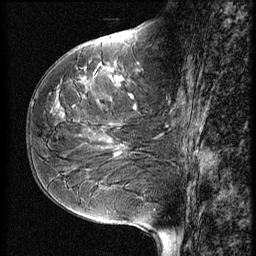
Breast MRI (dynamic contrast-enhanced), one sagittal slice; position 28 of 56 along the scan axis; 3 images stored at this slice position (order not interpretable as contrast timing); 1.5 T; TE 4.2 ms, TR 9 ms; 256 × 256 image matrix, field of view 180 × 180 mm. Patient: female, 51 years. From the clinical record (not read from this slice): setting: breast cancer imaged before/during neoadjuvant chemotherapy; receptor status: HR-positive, HER2-negative.
Annotated regions visible in this slice (semi-automatically segmented with operator editing):
- analysis volume of interest (the breast-tissue region the enhancement analysis was run in; not a lesion): bounding box <41,58,167,161> (left, top, right, bottom; pixels)
- tumour enhancement mask (voxels above the 140 % enhancement threshold inside the analysis volume of interest): <73,80,86,108>